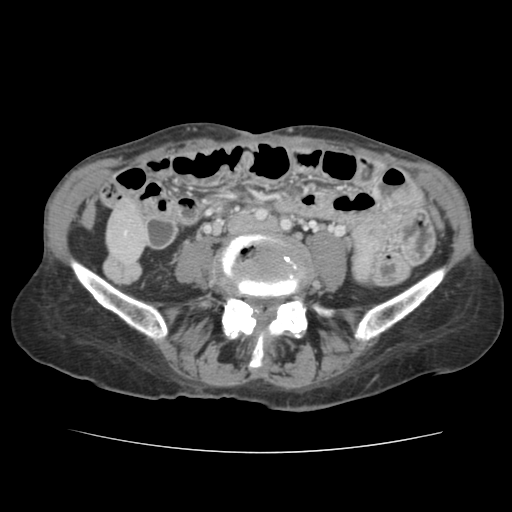
Contrast-enhanced abdominal CT, one axial slice; position 13 of 136 along the scan axis; 120 kVp; soft-tissue window (W 400 / L 40 HU); 512 × 512 image matrix, field of view 319 × 319 mm. Female patient, age 77 years. Case-level facts recorded for this patient, not image findings: diagnosis: colorectal cancer liver metastases, imaged before liver resection; multiple liver metastases: yes; largest metastasis: 3 cm; disease in both lobes: no.
Structures marked on this image (manually delineated by an expert):
- liver: bounding box <109,208,145,262> (left, top, right, bottom; pixels)